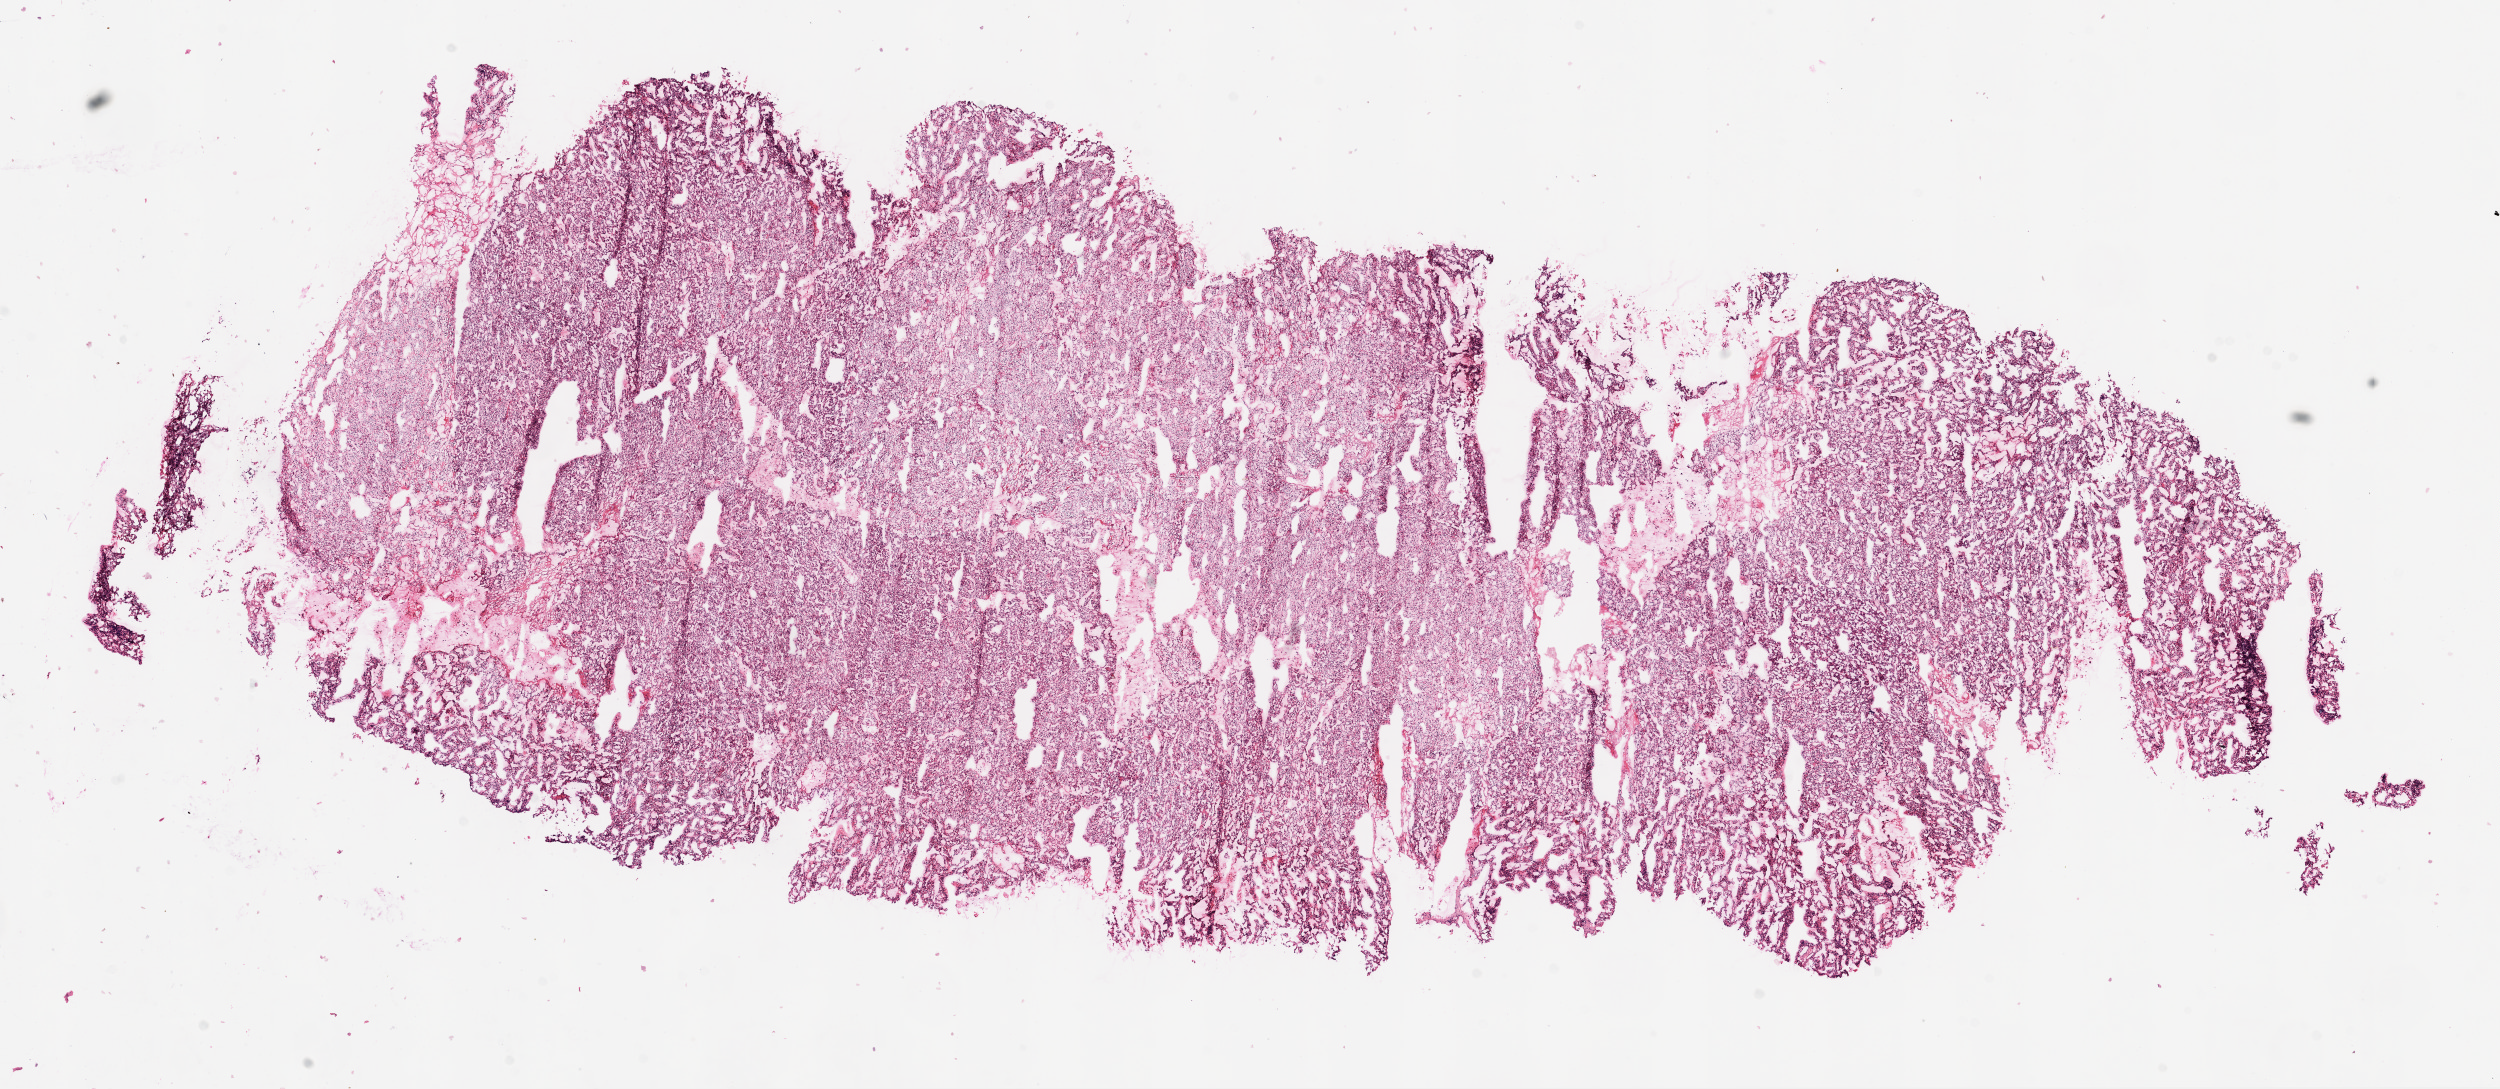
Digitized H&E-stained tissue section (whole slide) — whole scanned area (about 20.1 x 8.7 mm, from a 20x scan) shown as a low-resolution overview, frozen section from the top of the tissue portion, primary tumour sample from the kidney. Female patient; age at initial diagnosis 71 years. Histologic grade: G2 (moderately differentiated). Slide review estimates, as recorded: tumour cells 95%, tumour nuclei 90%, normal cells 0%, stromal cells 5%, necrosis 0%.
- laterality: left
- AJCC pathologic stage: III
- diagnosis: Clear cell adenocarcinoma, NOS